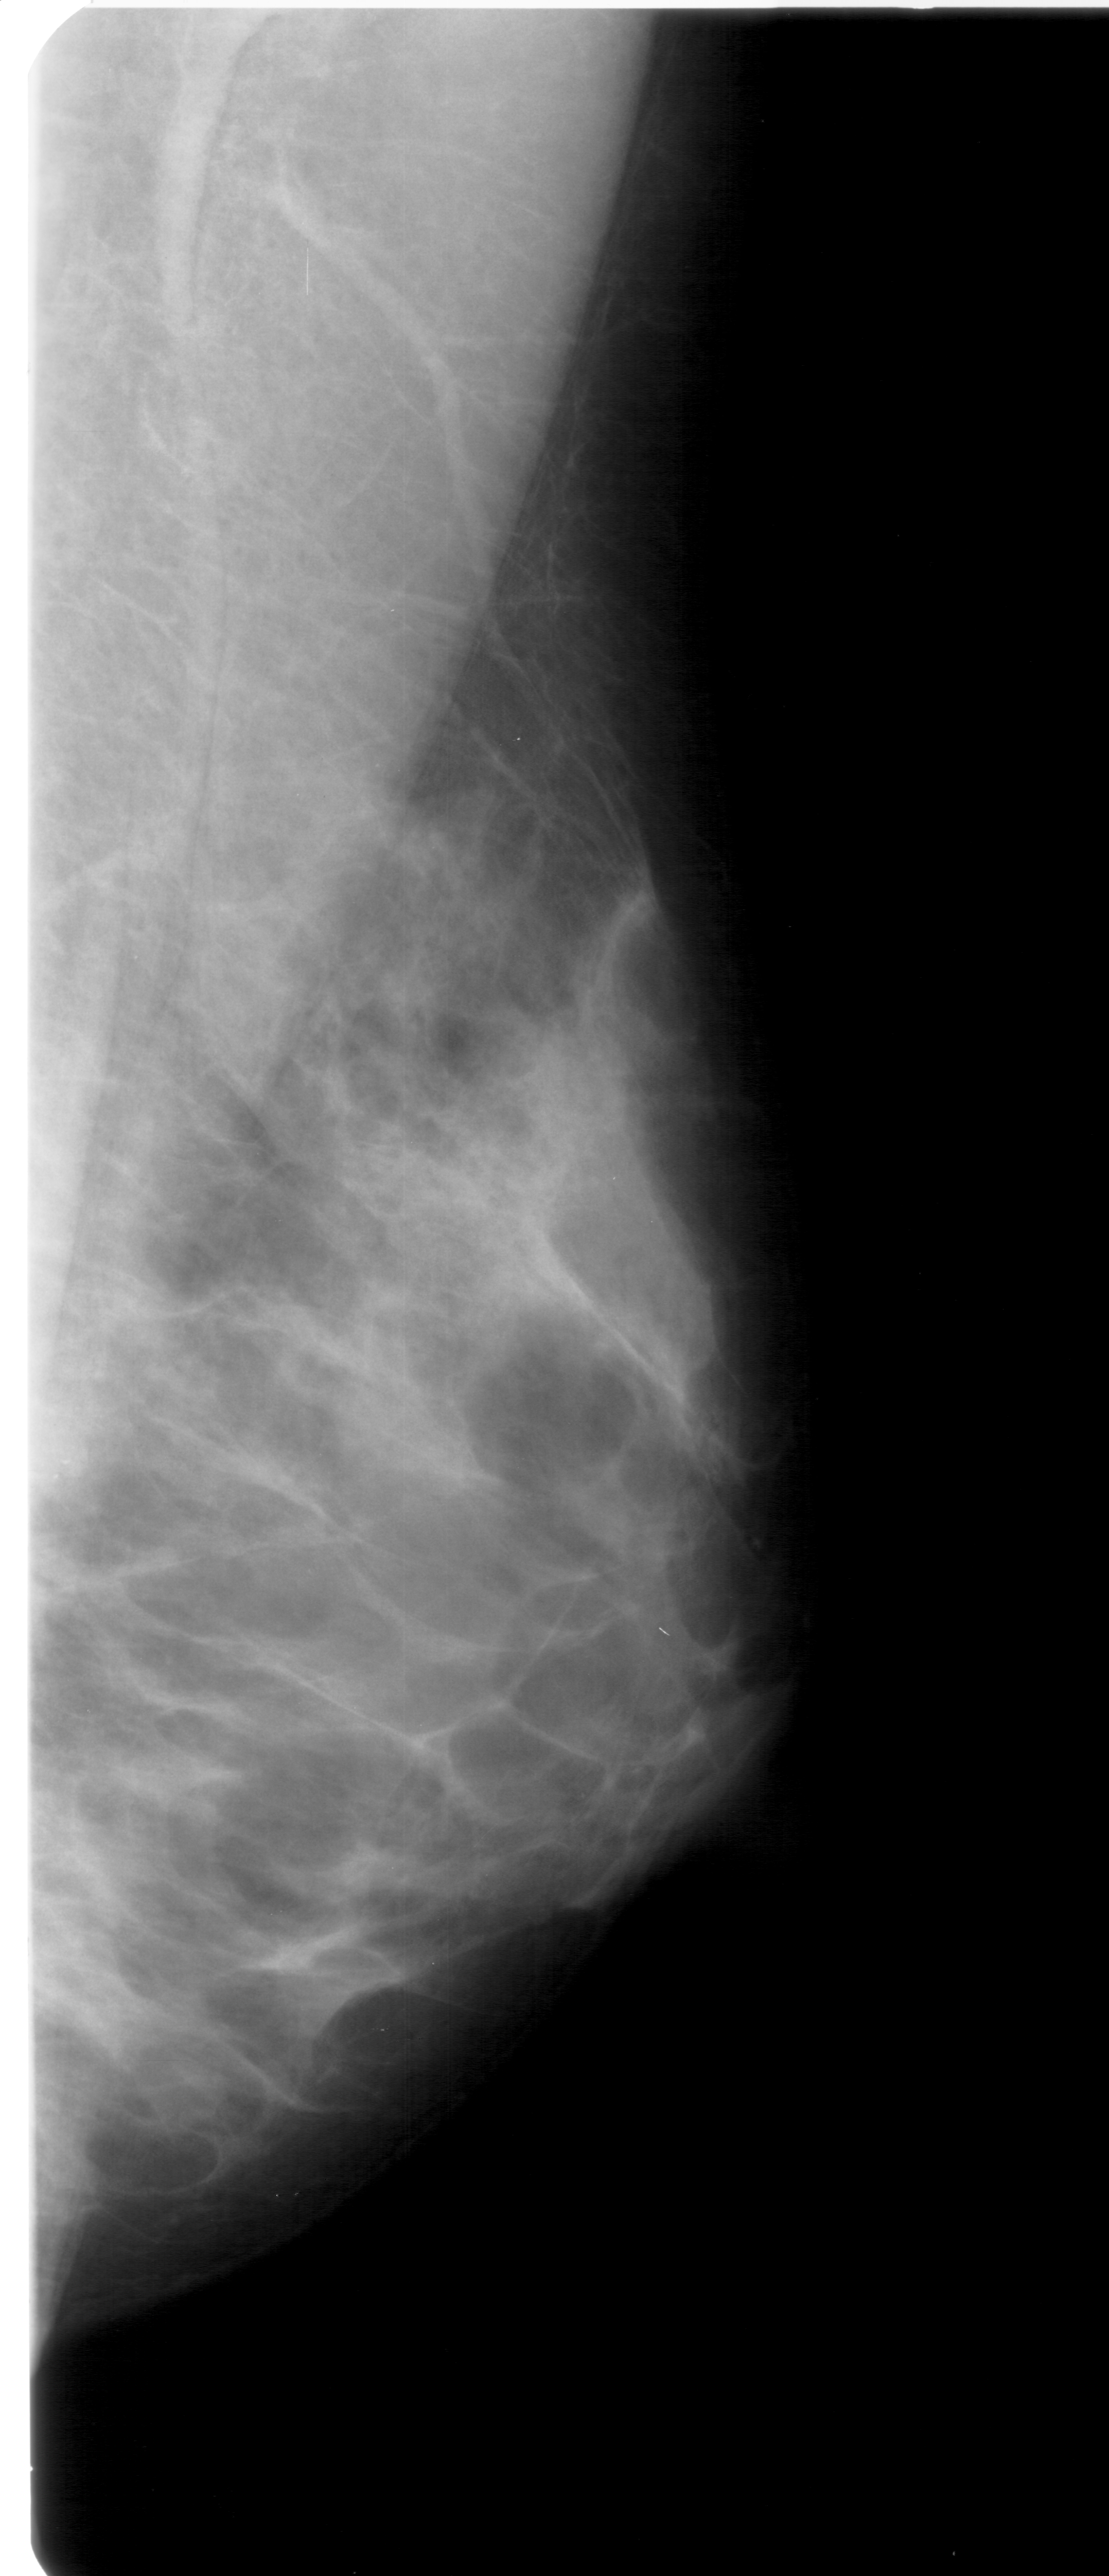
Scanned film-screen mammogram; right breast; MLO view; BI-RADS breast density category 4 (scale 1–4); 1109 × 2576 image matrix.
Marked abnormalities (boxes around the expert regions of interest):
- calcifications, morphology pleomorphic, distribution clustered; BI-RADS assessment category 4; pathology (as recorded): benign: bounding box <36,1379,166,1556> (left, top, right, bottom; pixels)